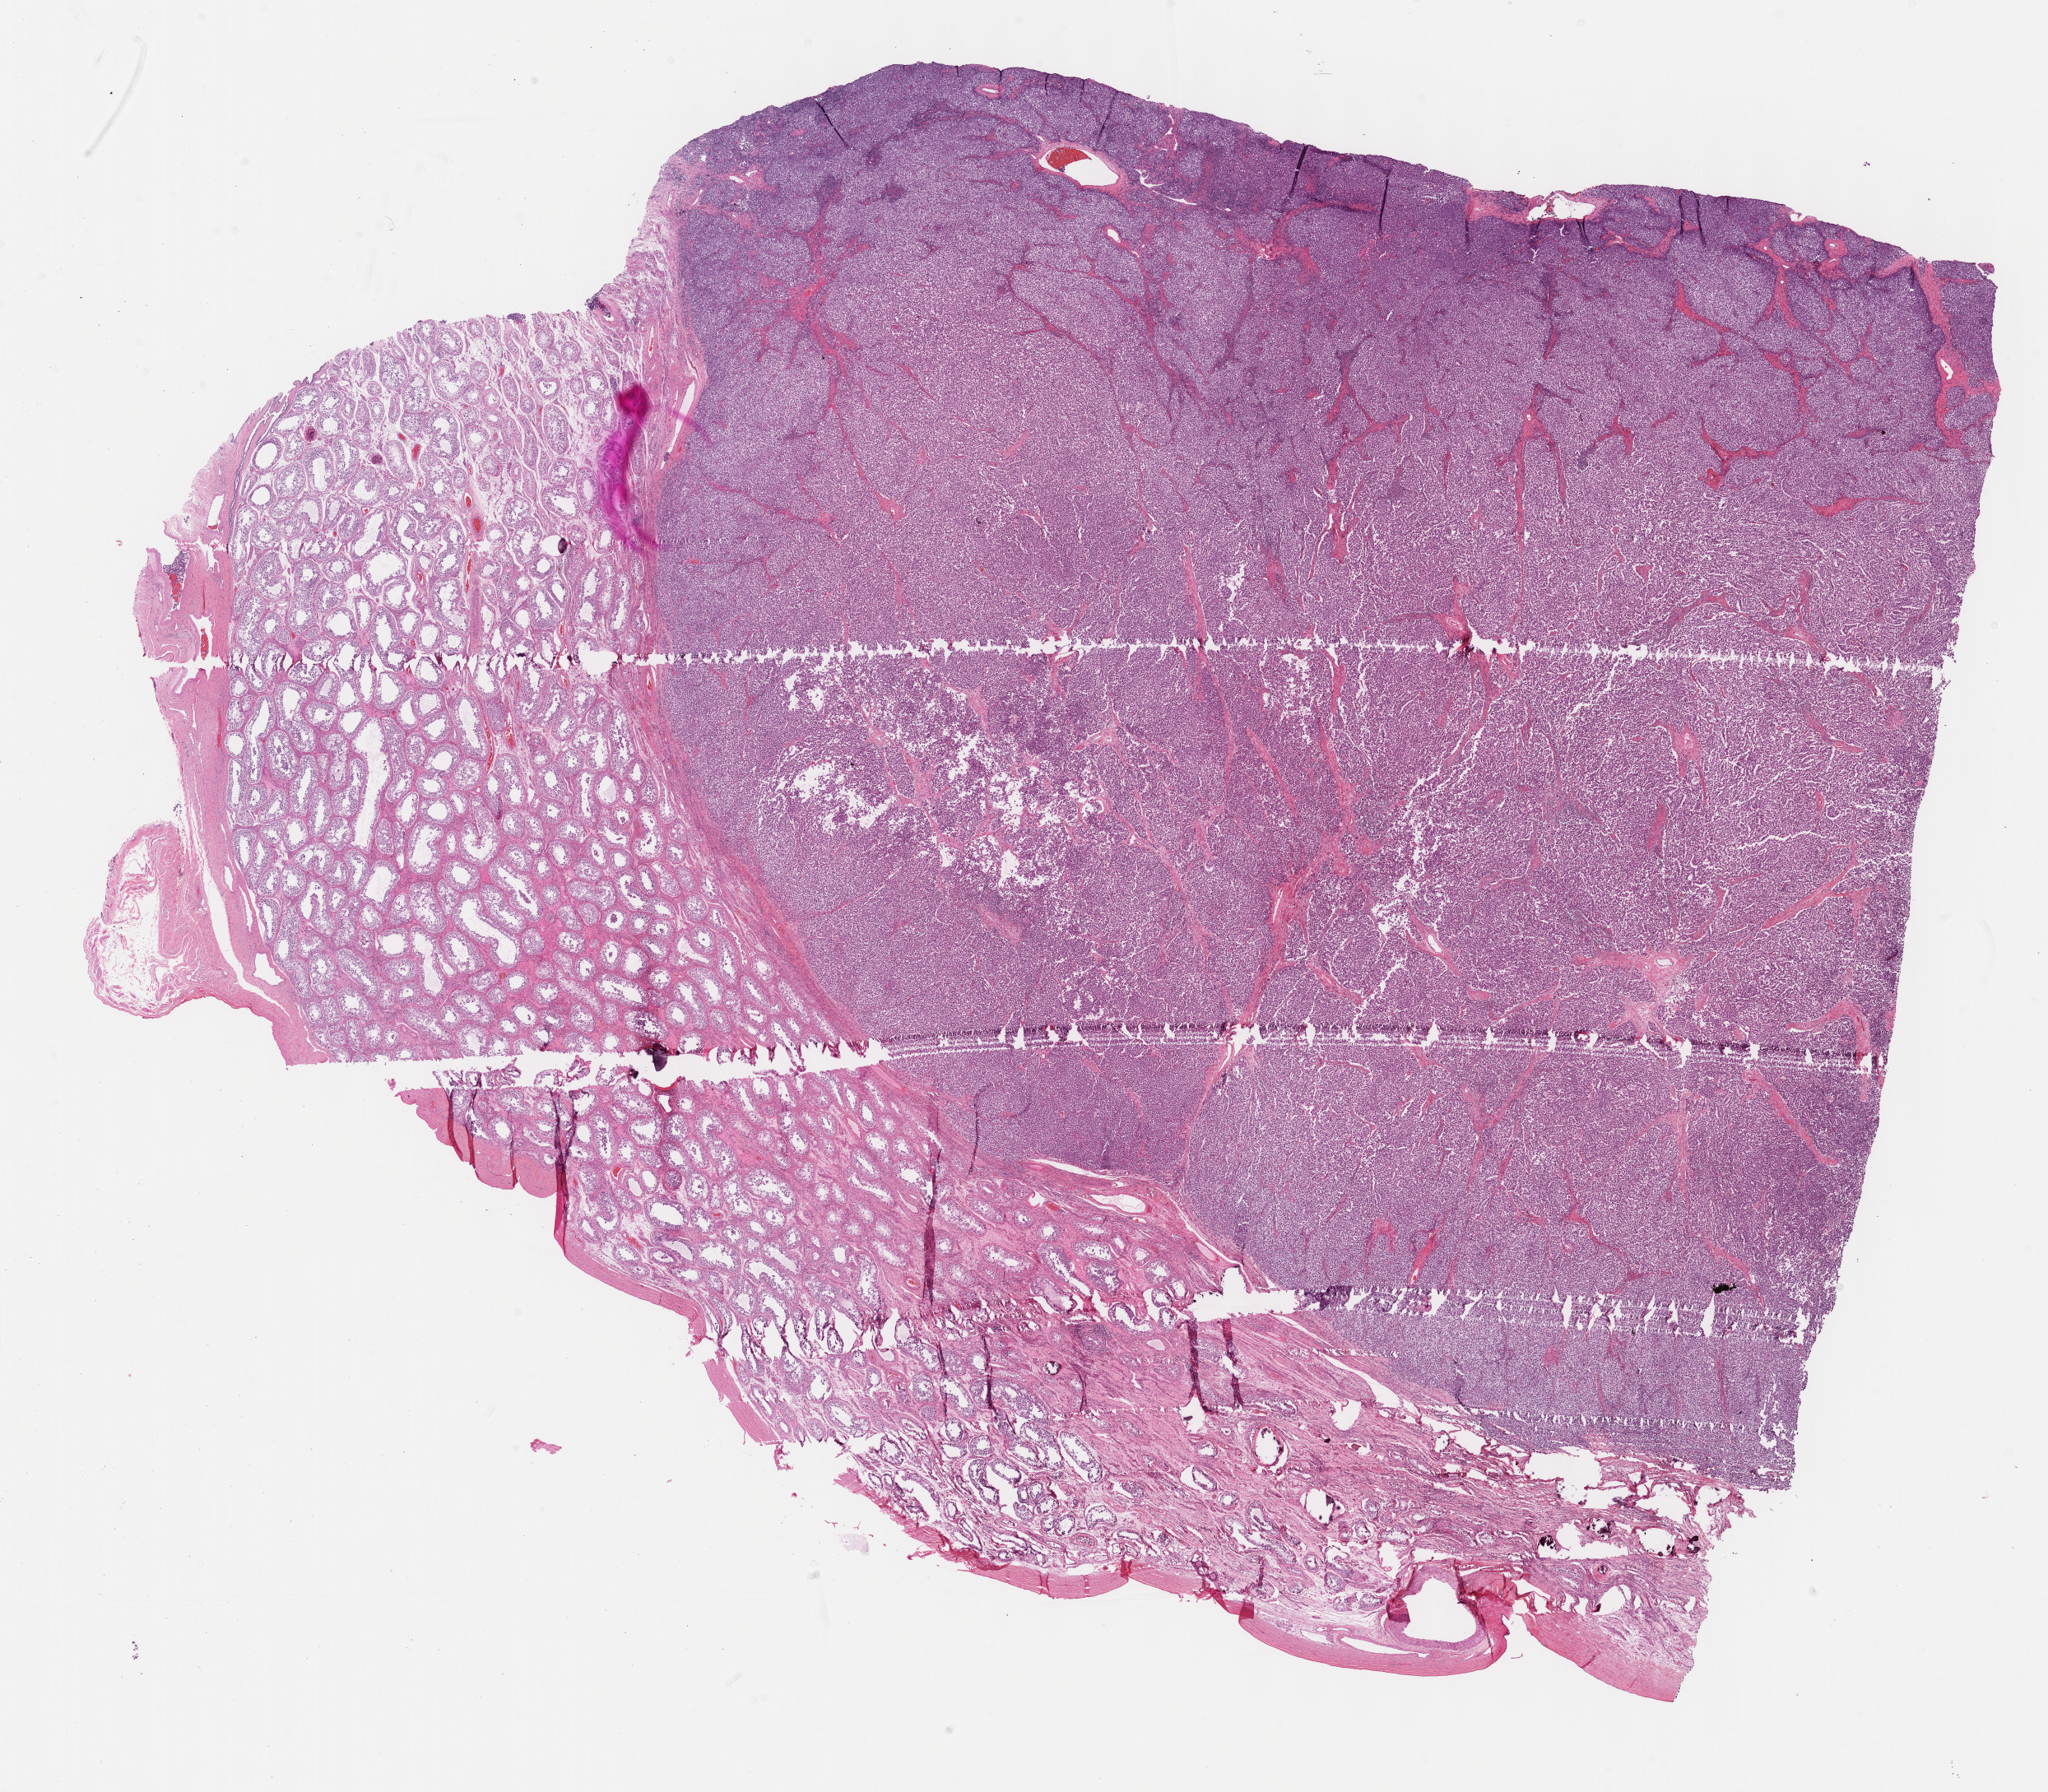
Digitized H&E-stained tissue section (whole slide), a low-resolution overview of the entire scanned area, about 20.1 x 17.6 mm; formalin-fixed paraffin-embedded (FFPE) diagnostic section; testis, primary tumour sample. Male patient; age at initial diagnosis 38 years.
• histologic diagnosis: Seminoma, NOS
• laterality: left